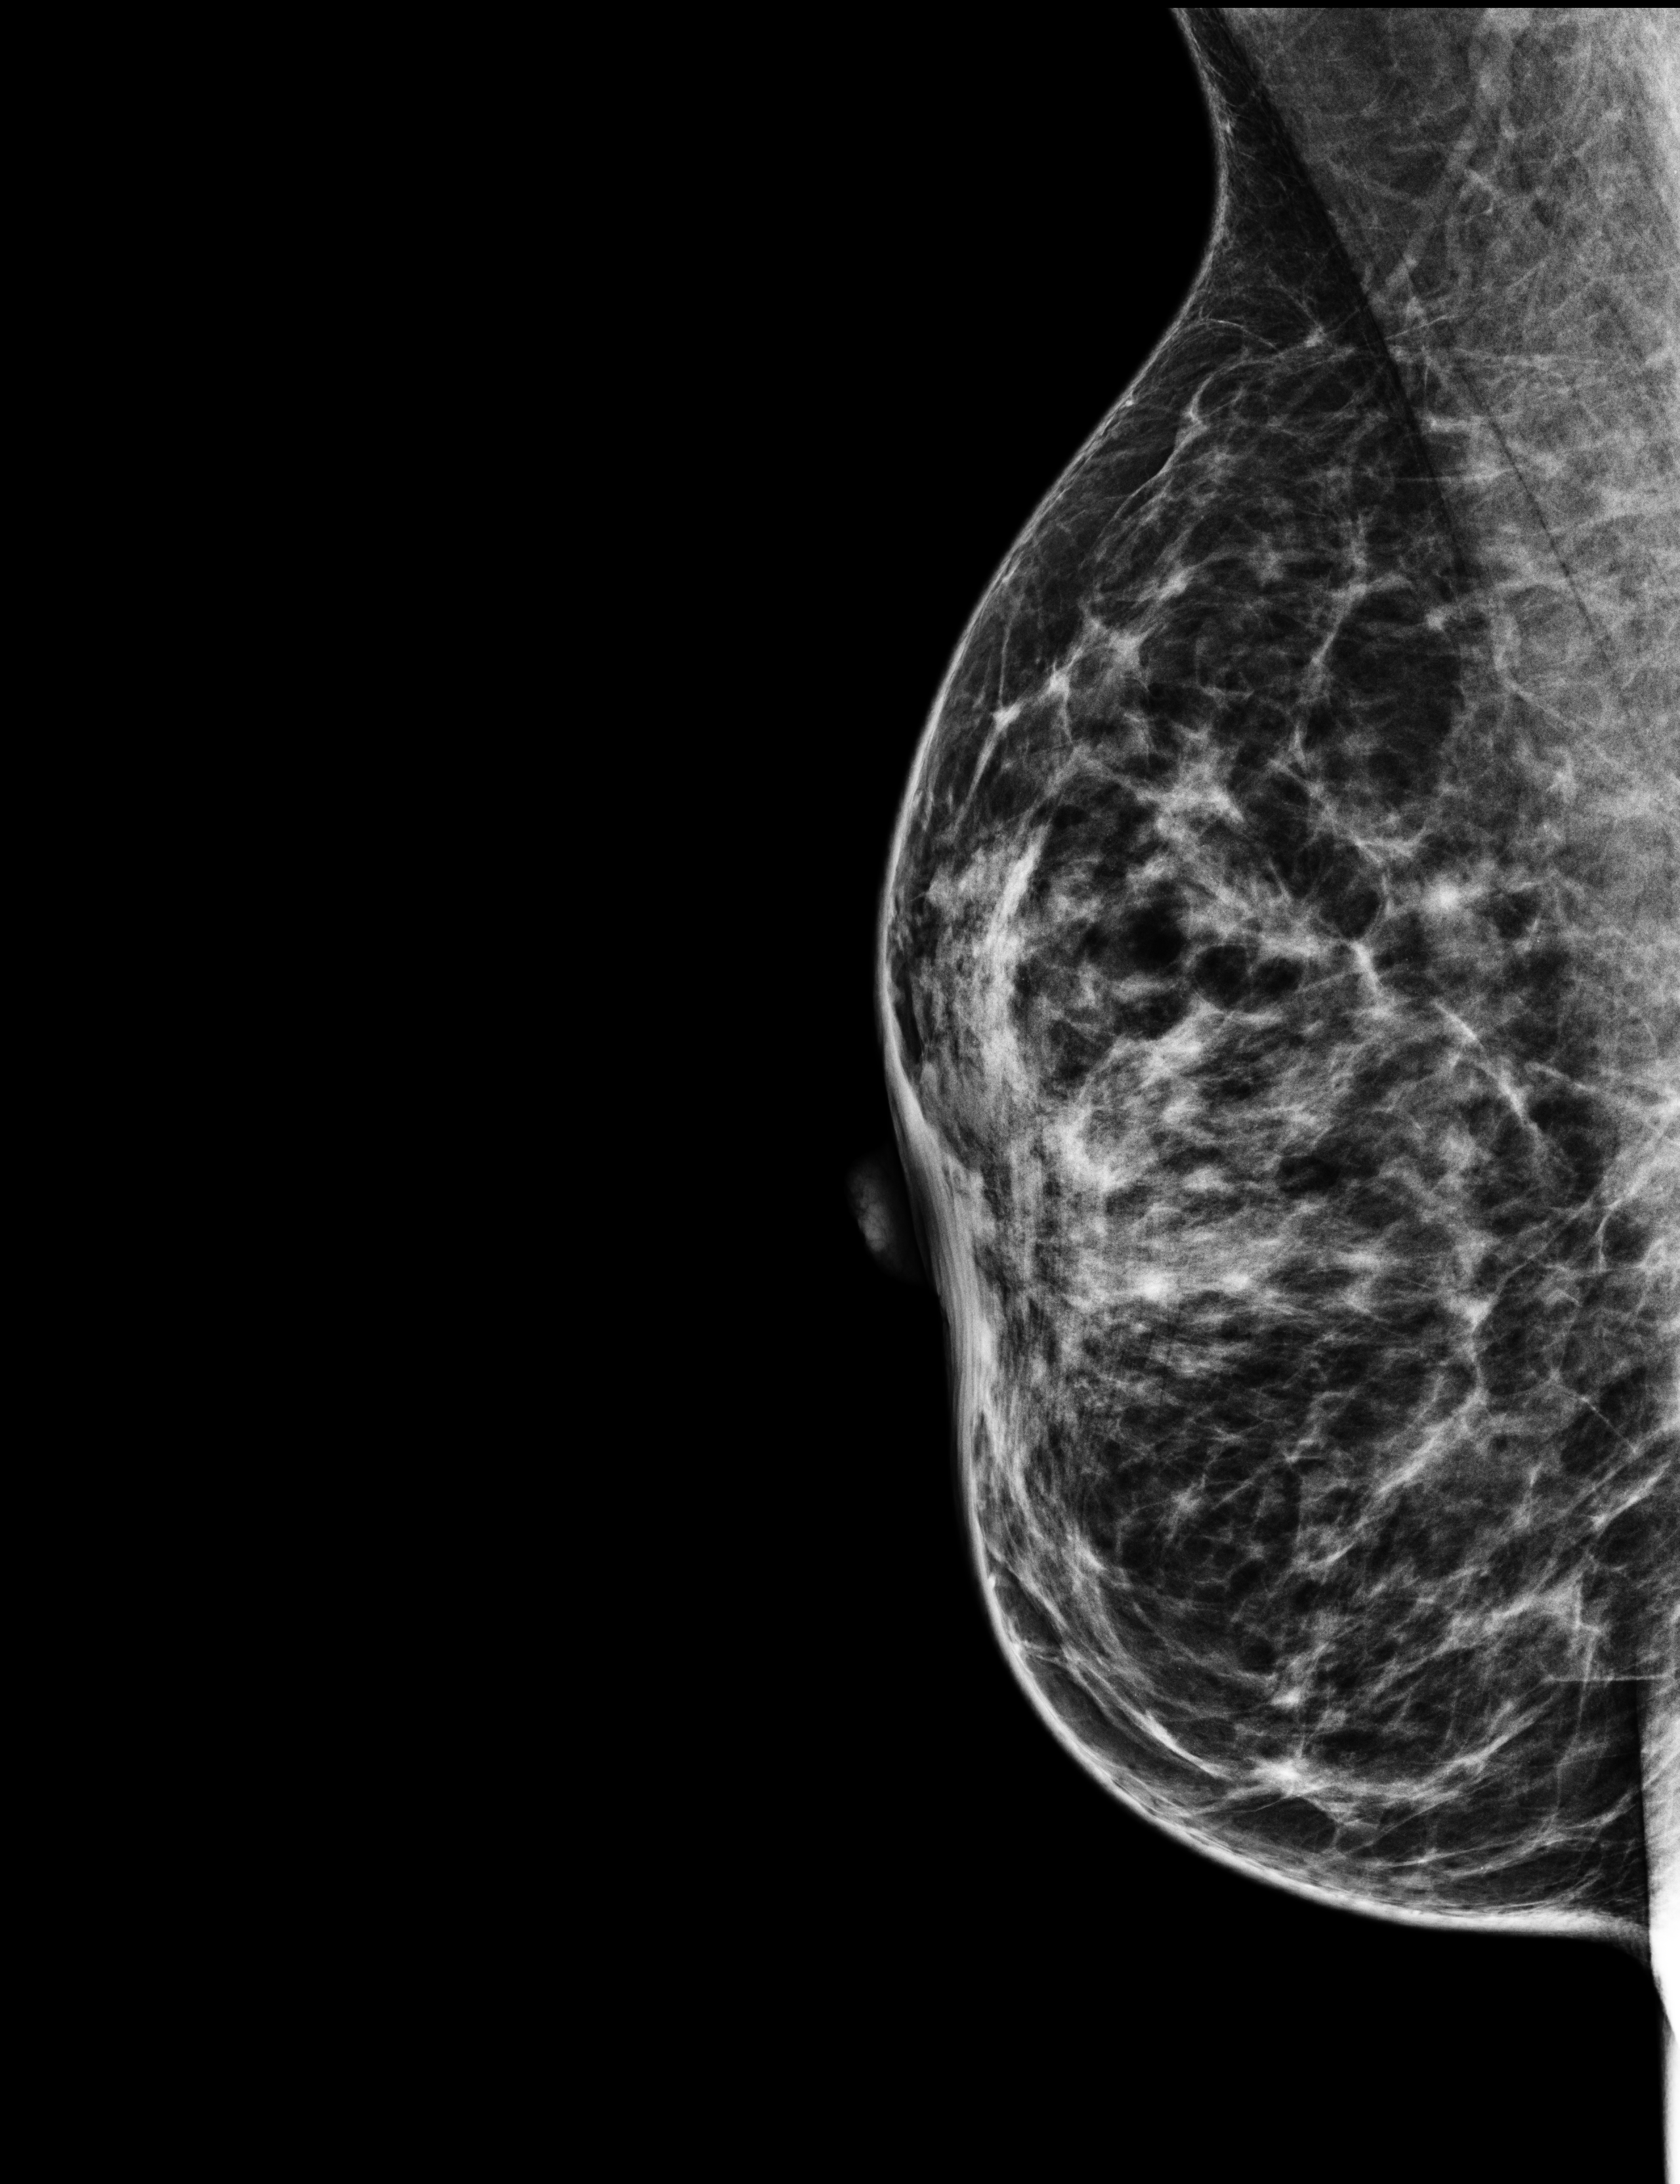
Annual screening mammography examination, compressed breast thickness 53 mm, system: Selenia Dimensions. Patient: female, 43 years.
Image type: full-field digital mammogram. Breast: right. Projection: mediolateral oblique (MLO) view.